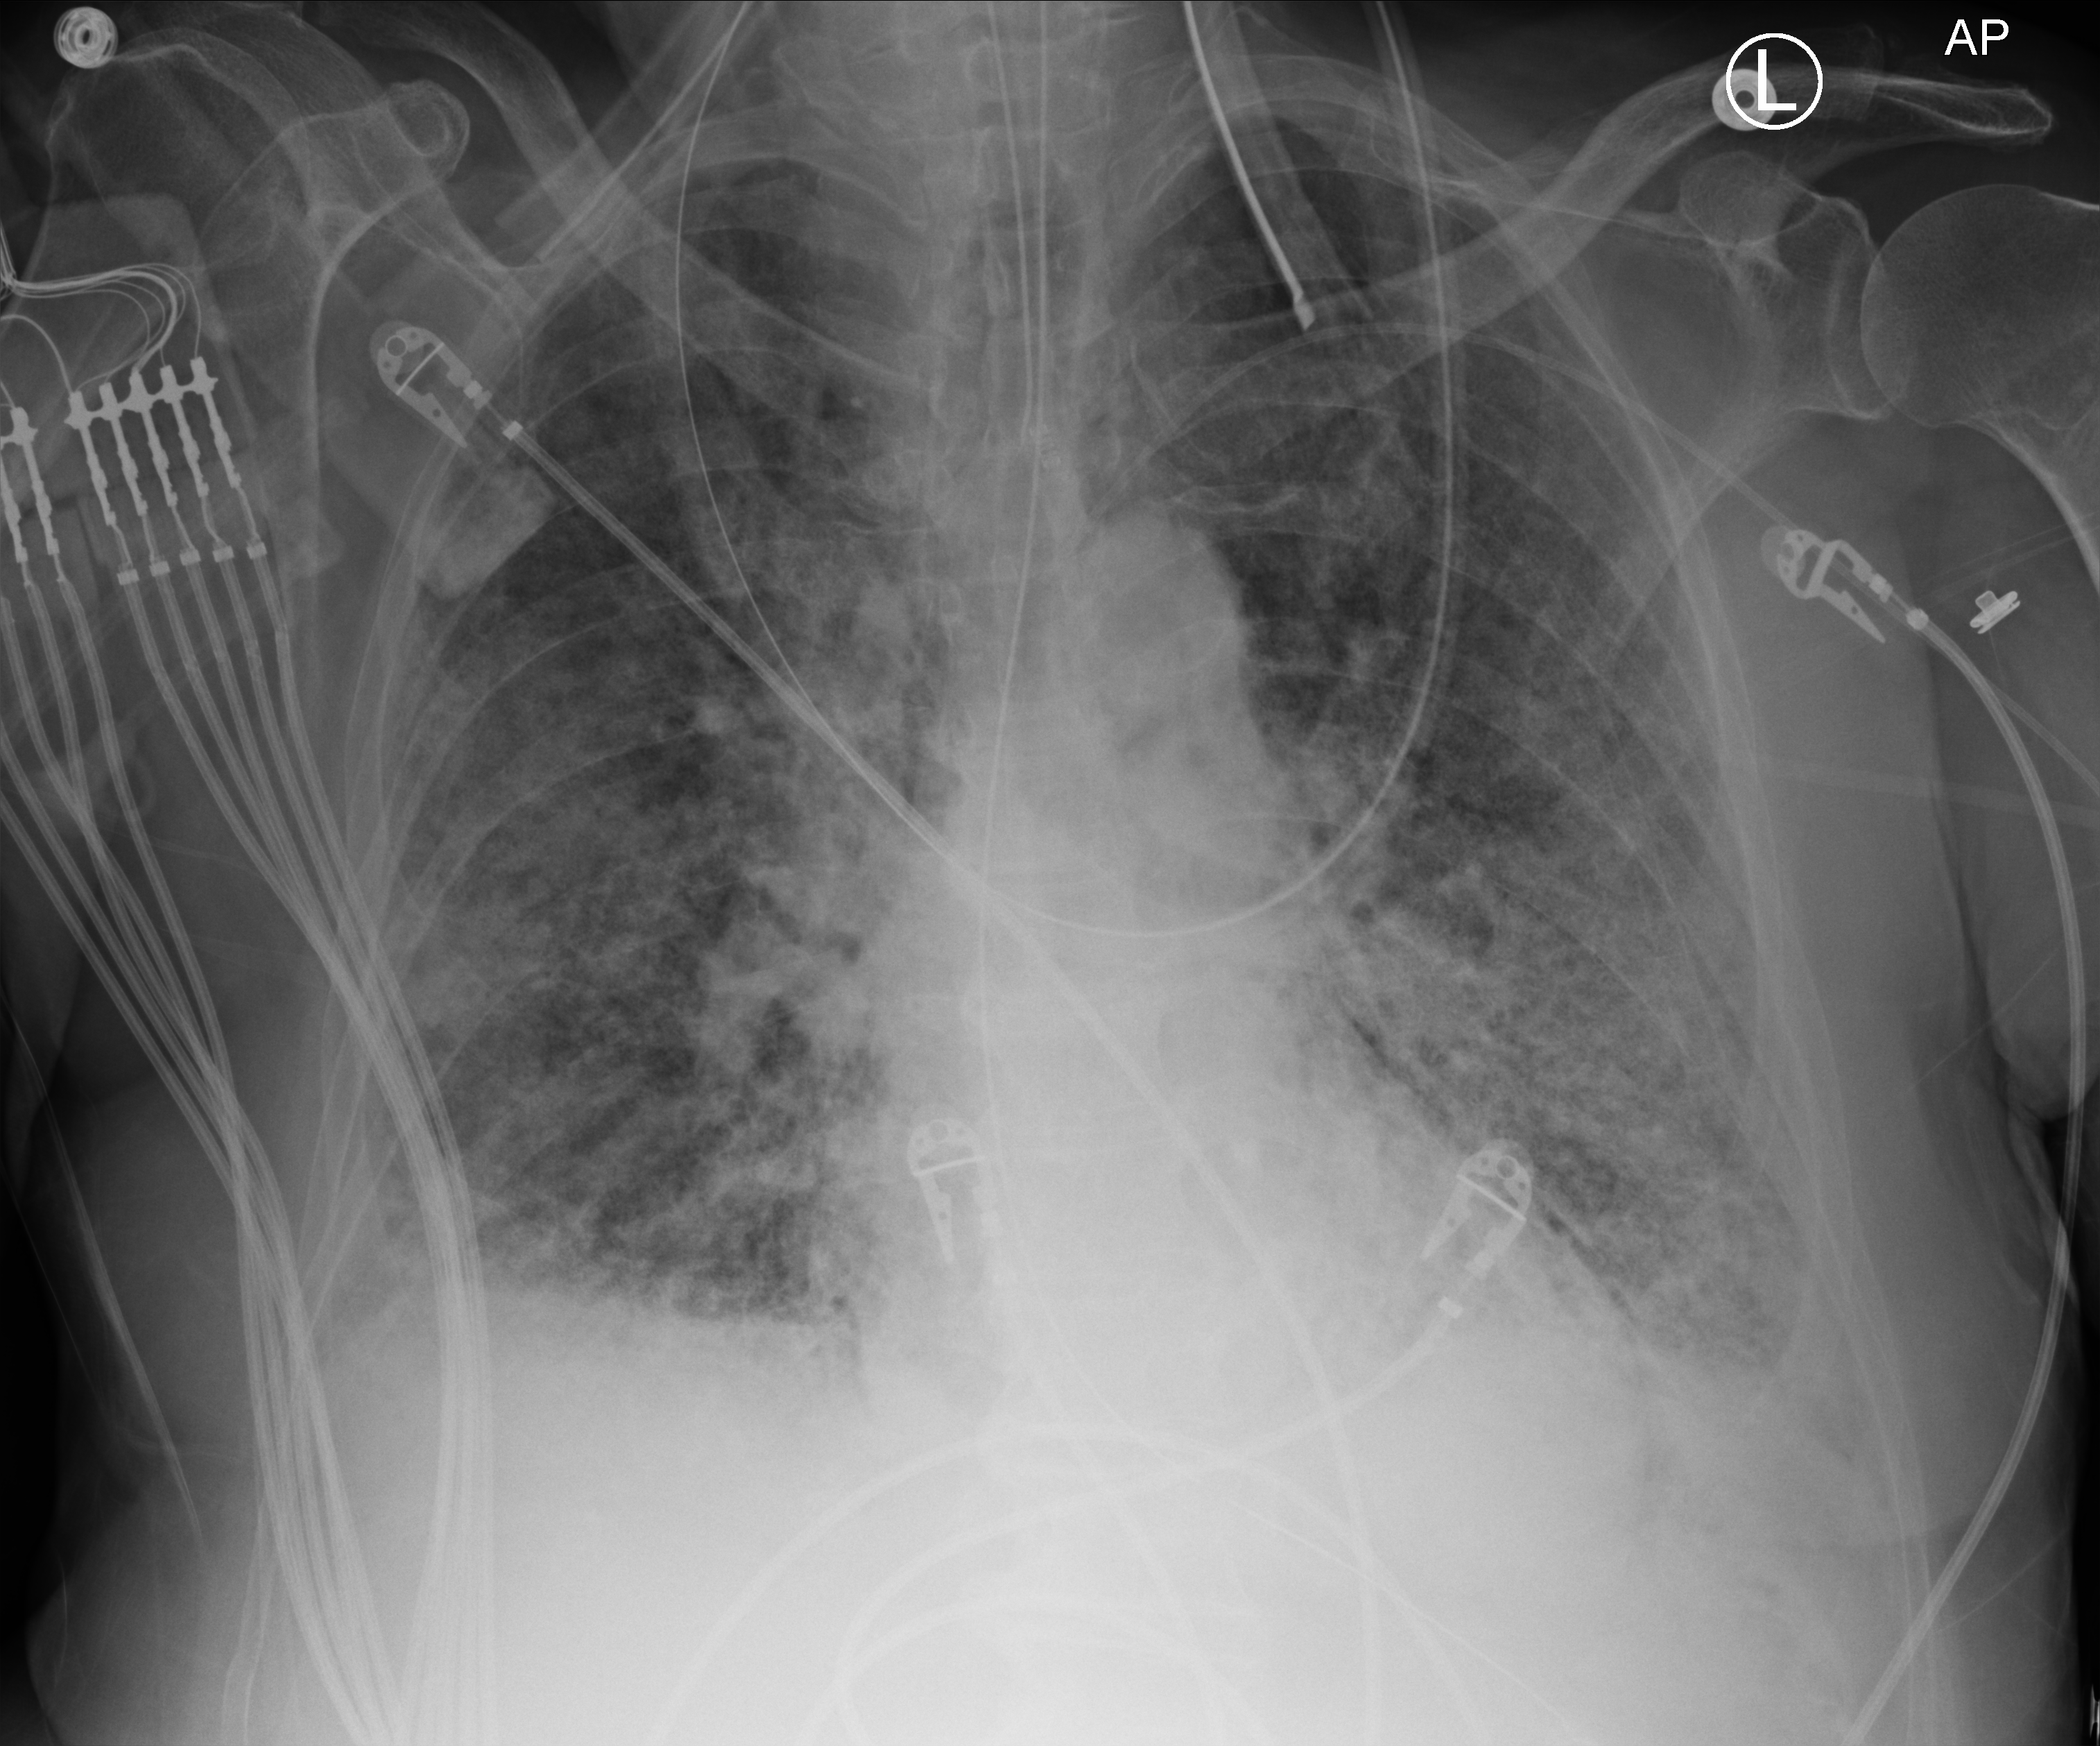
Chest X-ray (portable); anteroposterior (AP) projection. Male patient hospitalised with COVID-19, age 75–90 years.
Hospital-stay facts (about this admission, not read from this image; timing relative to this image not recorded):
- length of hospital stay: 47 days
- hypertension (admission record): no
- admitted to intensive care during this hospital stay: yes